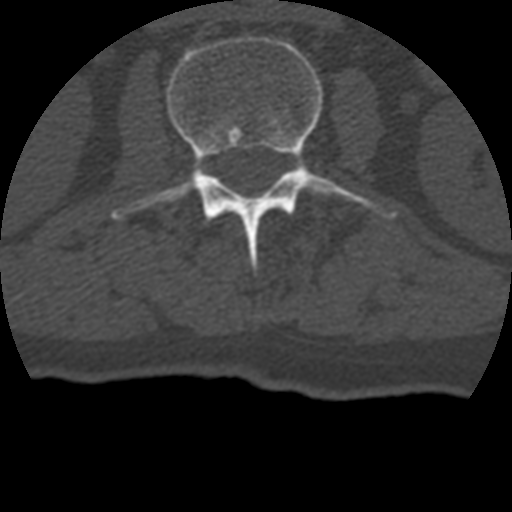
CT including the spine, one axial slice. Position 117 of 399 along the scan axis. 120 kVp. Bone window (W 1800 / L 400 HU). 1.25 mm slice thickness. 512 × 512 image matrix. Patient age 69 years. From the clinical record (not read from this slice): primary cancer: prostate.
Structures marked on this image (semi-automatic segmentation, software-assisted and operator-edited):
- L2 vertebra: bounding box [x1, y1, x2, y2] px = [114, 35, 393, 278]